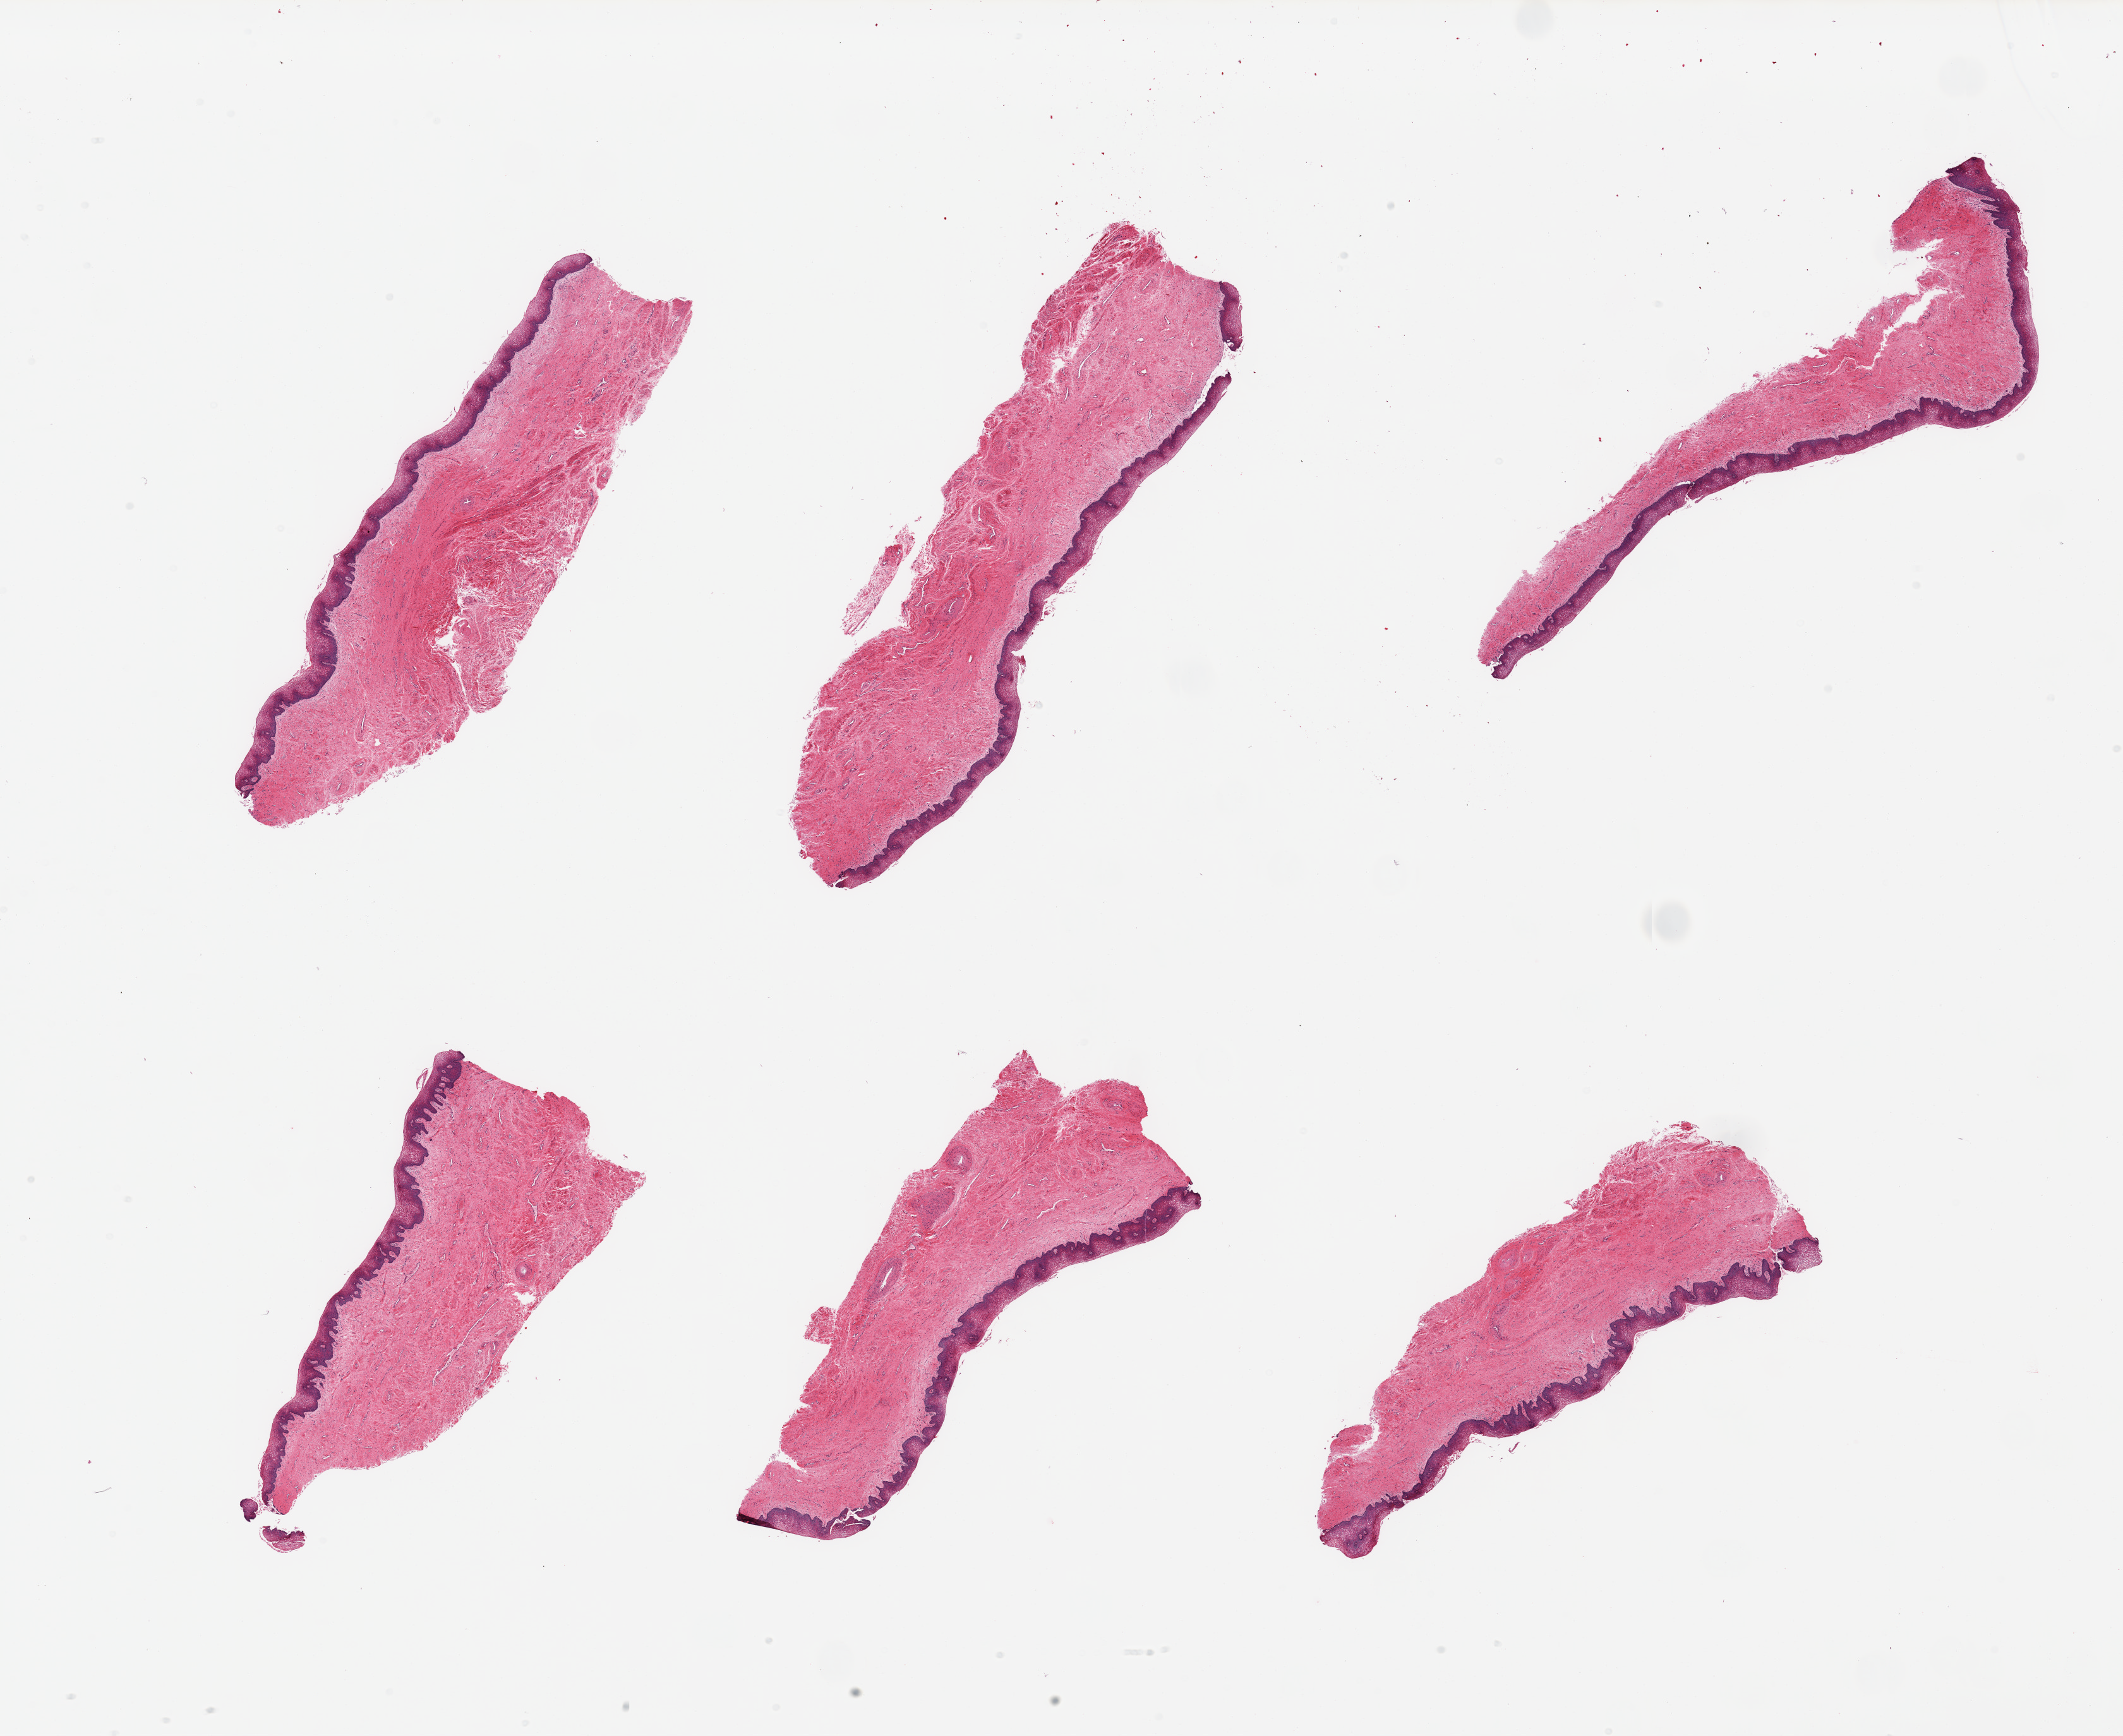
Digitized H&E-stained section, shown as a low-resolution overview of the whole scanned area (about 26.6 x 21.7 mm, acquisition: 20x scan). PAXgene-fixed, paraffin-embedded tissue. Target tissue: vagina. Donor tissue sample. Donor sex: female.
Review note (as recorded): 6 pieces; focally sloughed surface.